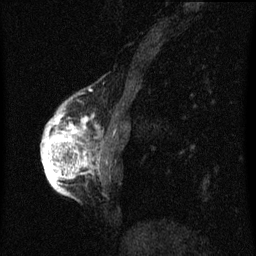
Breast MRI (dynamic contrast-enhanced), one sagittal slice. Position 17 of 60 along the scan axis. Dynamic contrast-enhanced series, image 2 of 3 at this slice position (ordered by acquisition). 1.5 T. TE 4.2 ms, TR 8 ms. 2 mm slice thickness. 256 × 256 image matrix, field of view 180 × 180 mm. Patient: female, 56 years.
Annotated regions visible in this slice (semi-automatically segmented with operator editing):
- analysis volume of interest (the breast-tissue region the enhancement analysis was run in; not a lesion): bounding box [x1, y1, x2, y2] px = [42, 110, 99, 193]
- tumour enhancement mask (voxels above the 70 % enhancement threshold inside the analysis volume of interest): [42, 116, 89, 193]